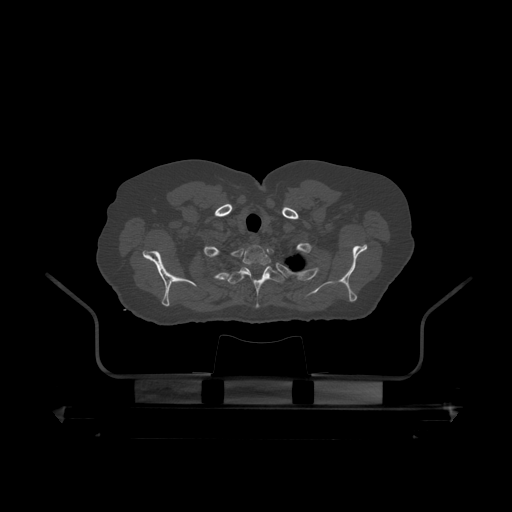
CT including the spine, one axial slice. Slice 382 of 390 in the series (ordered by position). 120 kVp. Bone window (W 1800 / L 400 HU). 1.25 mm slice thickness. 512 × 512 image matrix, field of view 650 × 650 mm. Patient: male, 60 years. From the clinical record (not read from this slice): primary cancer: prostate.
Outlined on this slice (semi-automatically segmented with operator editing):
- T1 vertebra: bounding box [x1, y1, x2, y2] px = [240, 246, 271, 272]
- T2 vertebra: [229, 265, 285, 310]